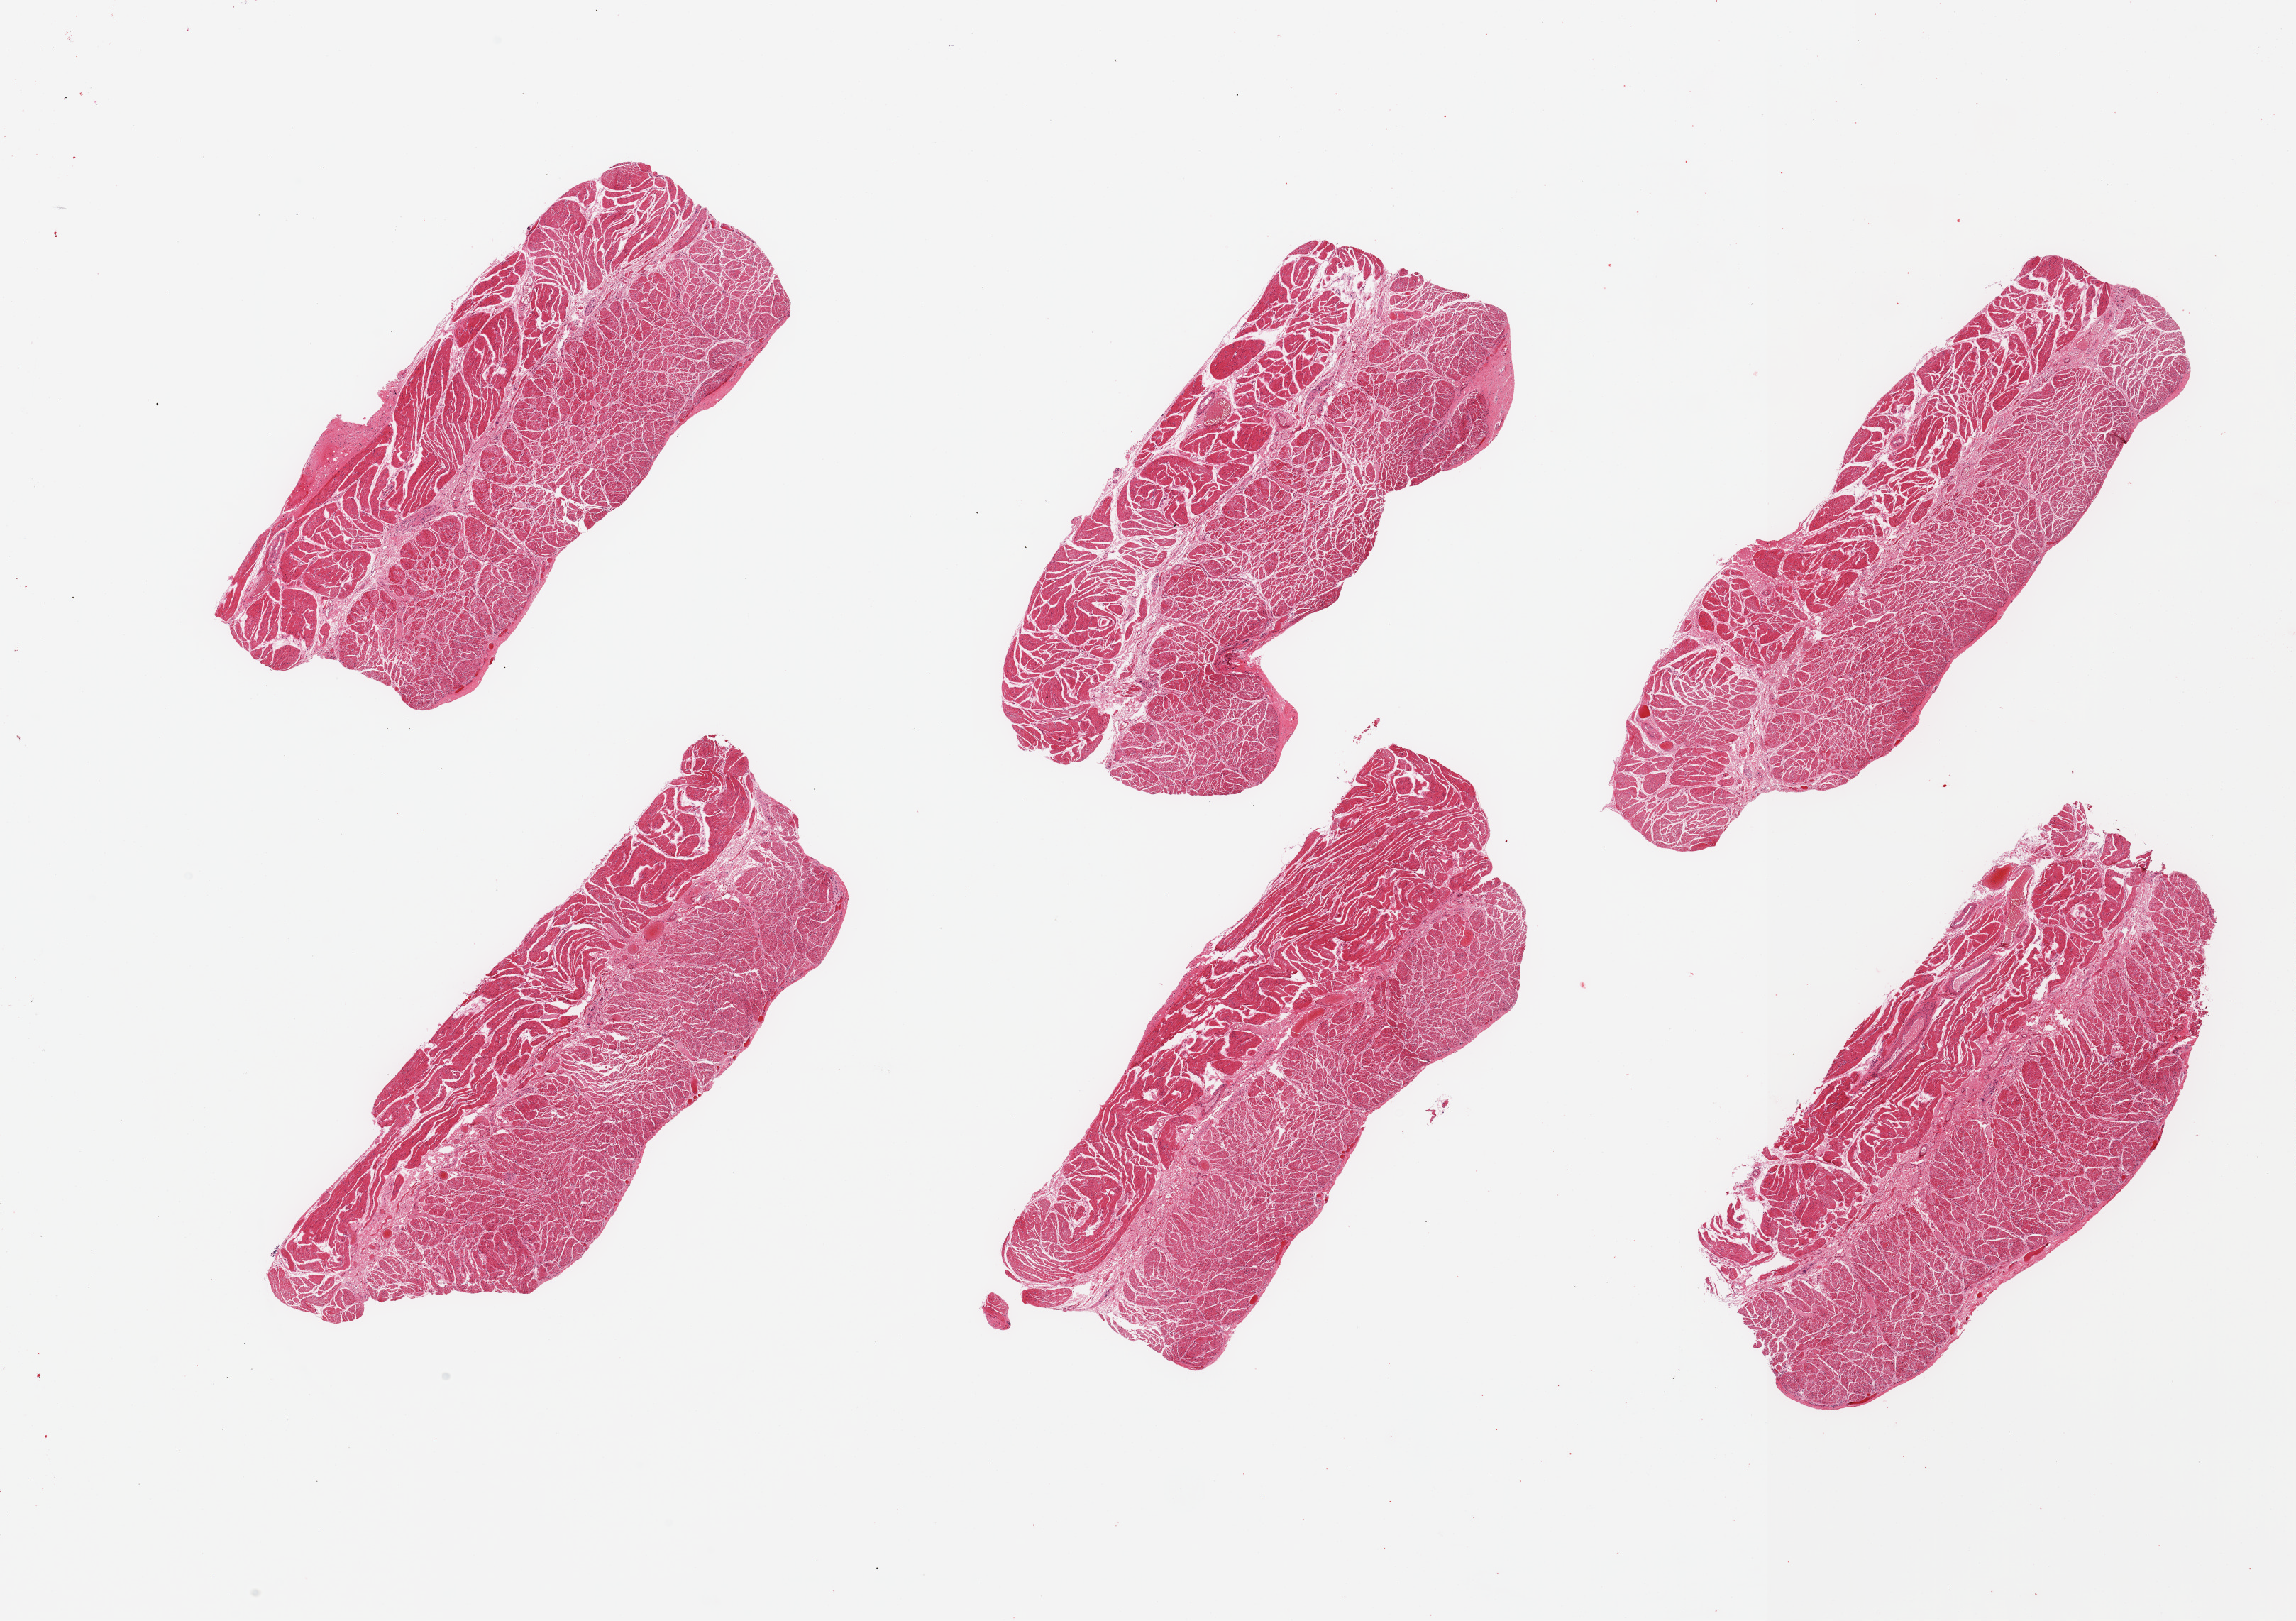
Digitized H&E-stained section — whole scanned area (about 25.6 x 18.1 mm) shown as a low-resolution overview; PAXgene-fixed, paraffin-embedded tissue; target tissue: esophageal muscle; tissue donor sample.
Review note (as recorded): 6 pieces; well dissected muscle.